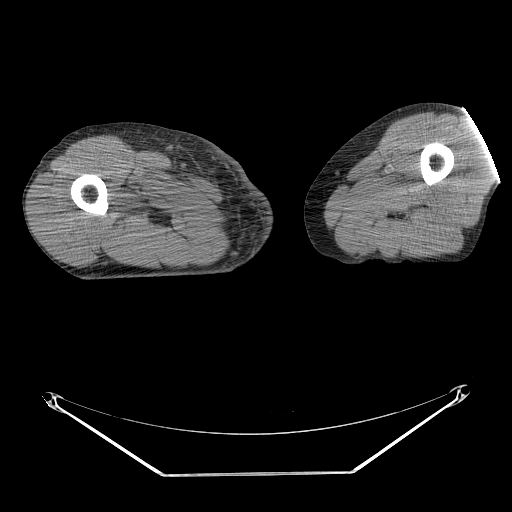
CT of an extremity soft-tissue mass (from a PET/CT study), one axial slice. Position 234 of 311 along the scan axis. 140 kVp. Soft-tissue window (W 400 / L 40 HU). 512 × 512 image matrix, field of view 500 × 500 mm. Male patient. From the clinical record (not read from this slice): histological type: undifferentiated - pleiomorphic; grade: high; site of the primary tumour: right thigh.
Annotated regions visible in this slice (expert contour drawn on MRI and transferred to this co-registered scan by the dataset authors):
- gross tumour volume including surrounding oedema: bounding box [x1, y1, x2, y2] px = [137, 192, 165, 216]